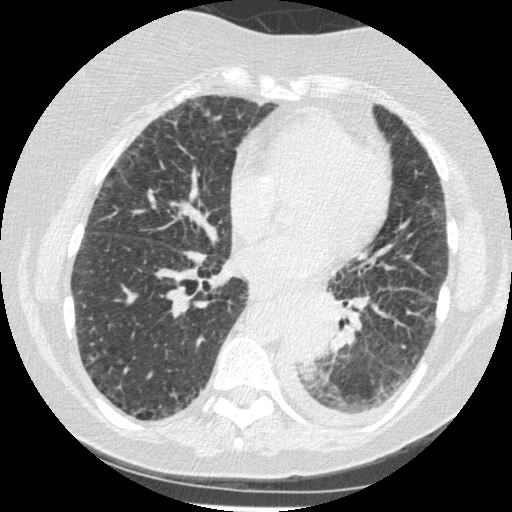
Axial slice from a low-dose chest CT screening exam, third screening round (two years after baseline), lung window (W 1500 / L -600 HU), 1.25 mm slice thickness, standard (soft-tissue) reconstruction kernel (STANDARD), 120 kVp, slice 245 of 341 in the series. Female, age 60 years at enrolment. Former smoker at enrolment.
Expert-annotated lung lesion, bounding box (x1, y1, x2, y2) in pixels: (277, 303, 343, 376). Screening reader's record for this exam (one nodule recorded; not confirmed to be the boxed lesion): non-calcified nodule or mass ≥4 mm, left lower lobe, 54 × 38 mm, smooth margins, soft tissue attenuation, pre-existing on the prior screen: yes; interval growth: yes. Official screen result: positive, other. Lung cancer was diagnosed 15 days after this screen: small cell carcinoma, NOS, left lower lobe, undifferentiated (G4), stage IV (AJCC 6th edition), 69 mm at pathology.